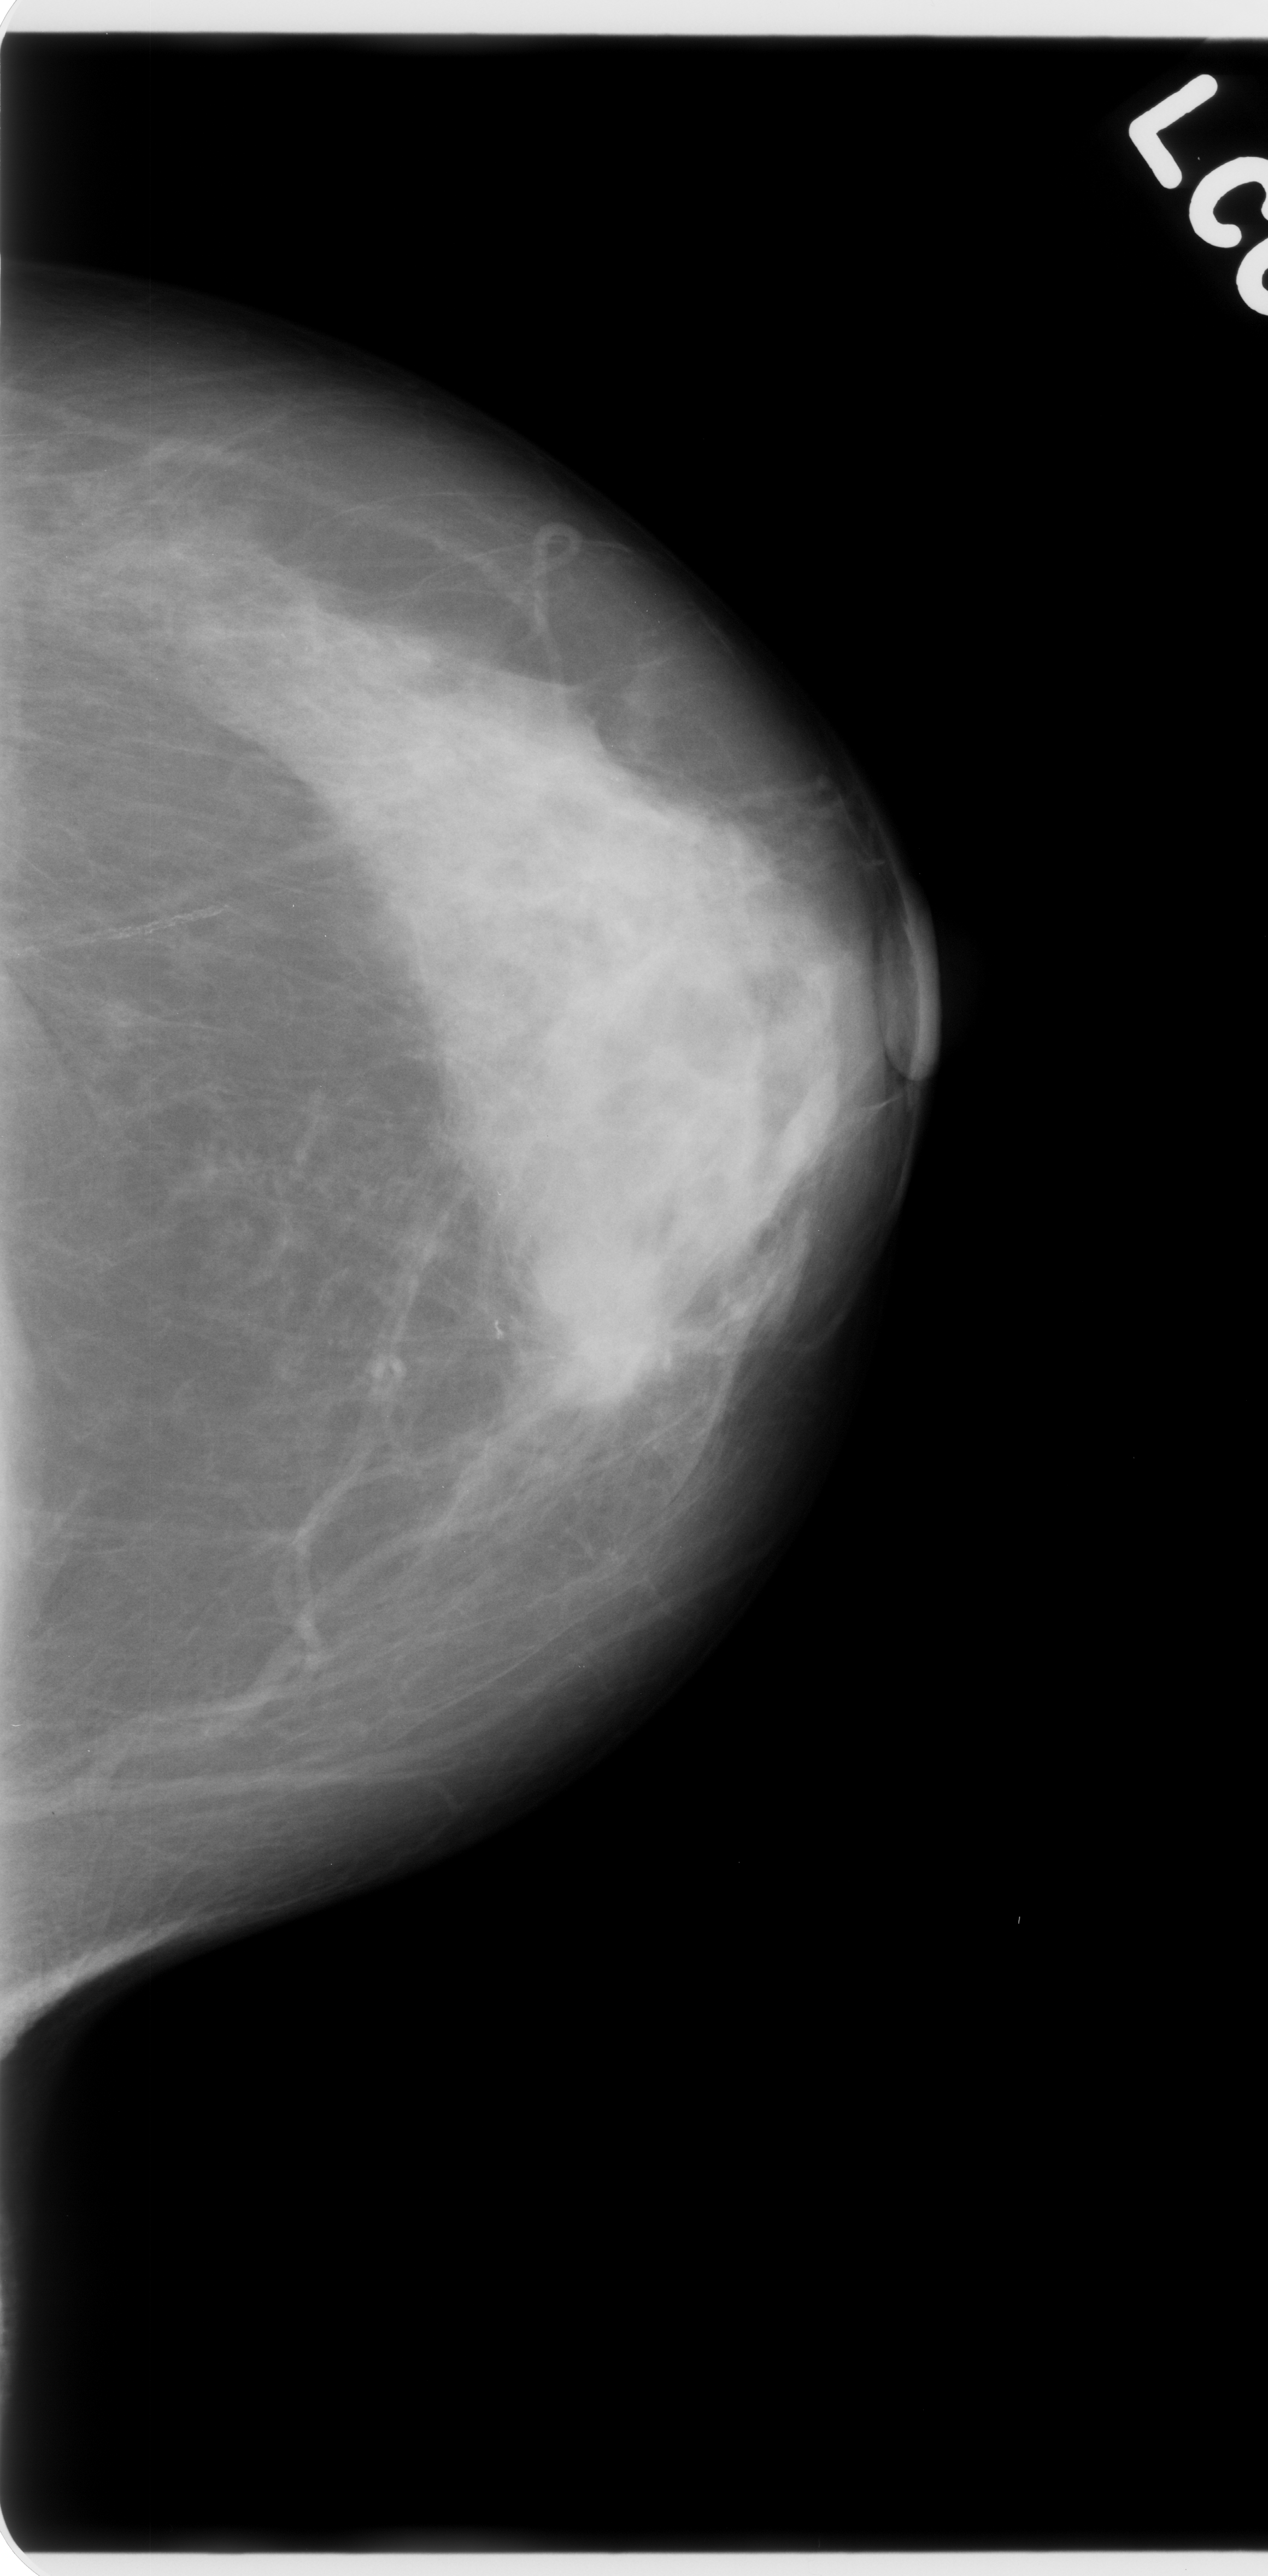
Scanned film-screen mammogram. Left breast. CC view. BI-RADS breast density category 3 (scale 1–4). 1268 × 2576 image matrix.
Expert-marked regions of interest on this film, with their recorded descriptors:
- mass, shape lobulated, margins spiculated; BI-RADS assessment category 5; pathology (as recorded): malignant: bounding box [x1, y1, x2, y2] px = [486, 1237, 695, 1436]